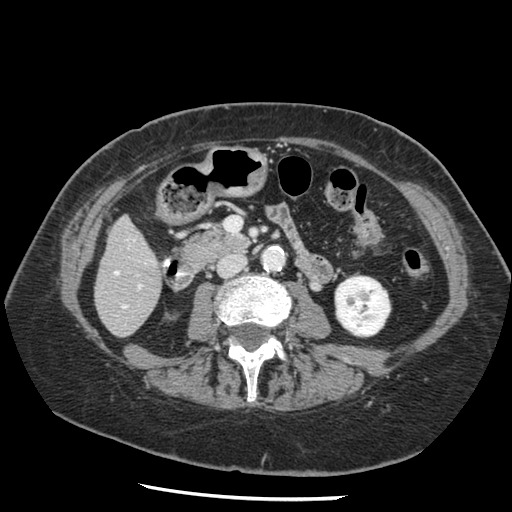
Contrast-enhanced abdominal CT, one axial slice; 120 kVp; soft-tissue window (W 400 / L 40 HU); 2.5 mm slice thickness; 512 × 512 image matrix, field of view 330 × 330 mm. Female patient, age 85 years. Case-level facts recorded for this patient, not image findings: diagnosis: colorectal cancer liver metastases, imaged before liver resection; multiple liver metastases: no; largest metastasis: 0.9 cm; chemotherapy before resection: yes.
Structures marked on this image (manually delineated by an expert):
- hepatic veins: bounding box [x1, y1, x2, y2] px = [114, 271, 126, 308]
- liver: [96, 218, 162, 336]
- planned liver remnant (the part of the liver to remain after resection): [96, 218, 162, 332]